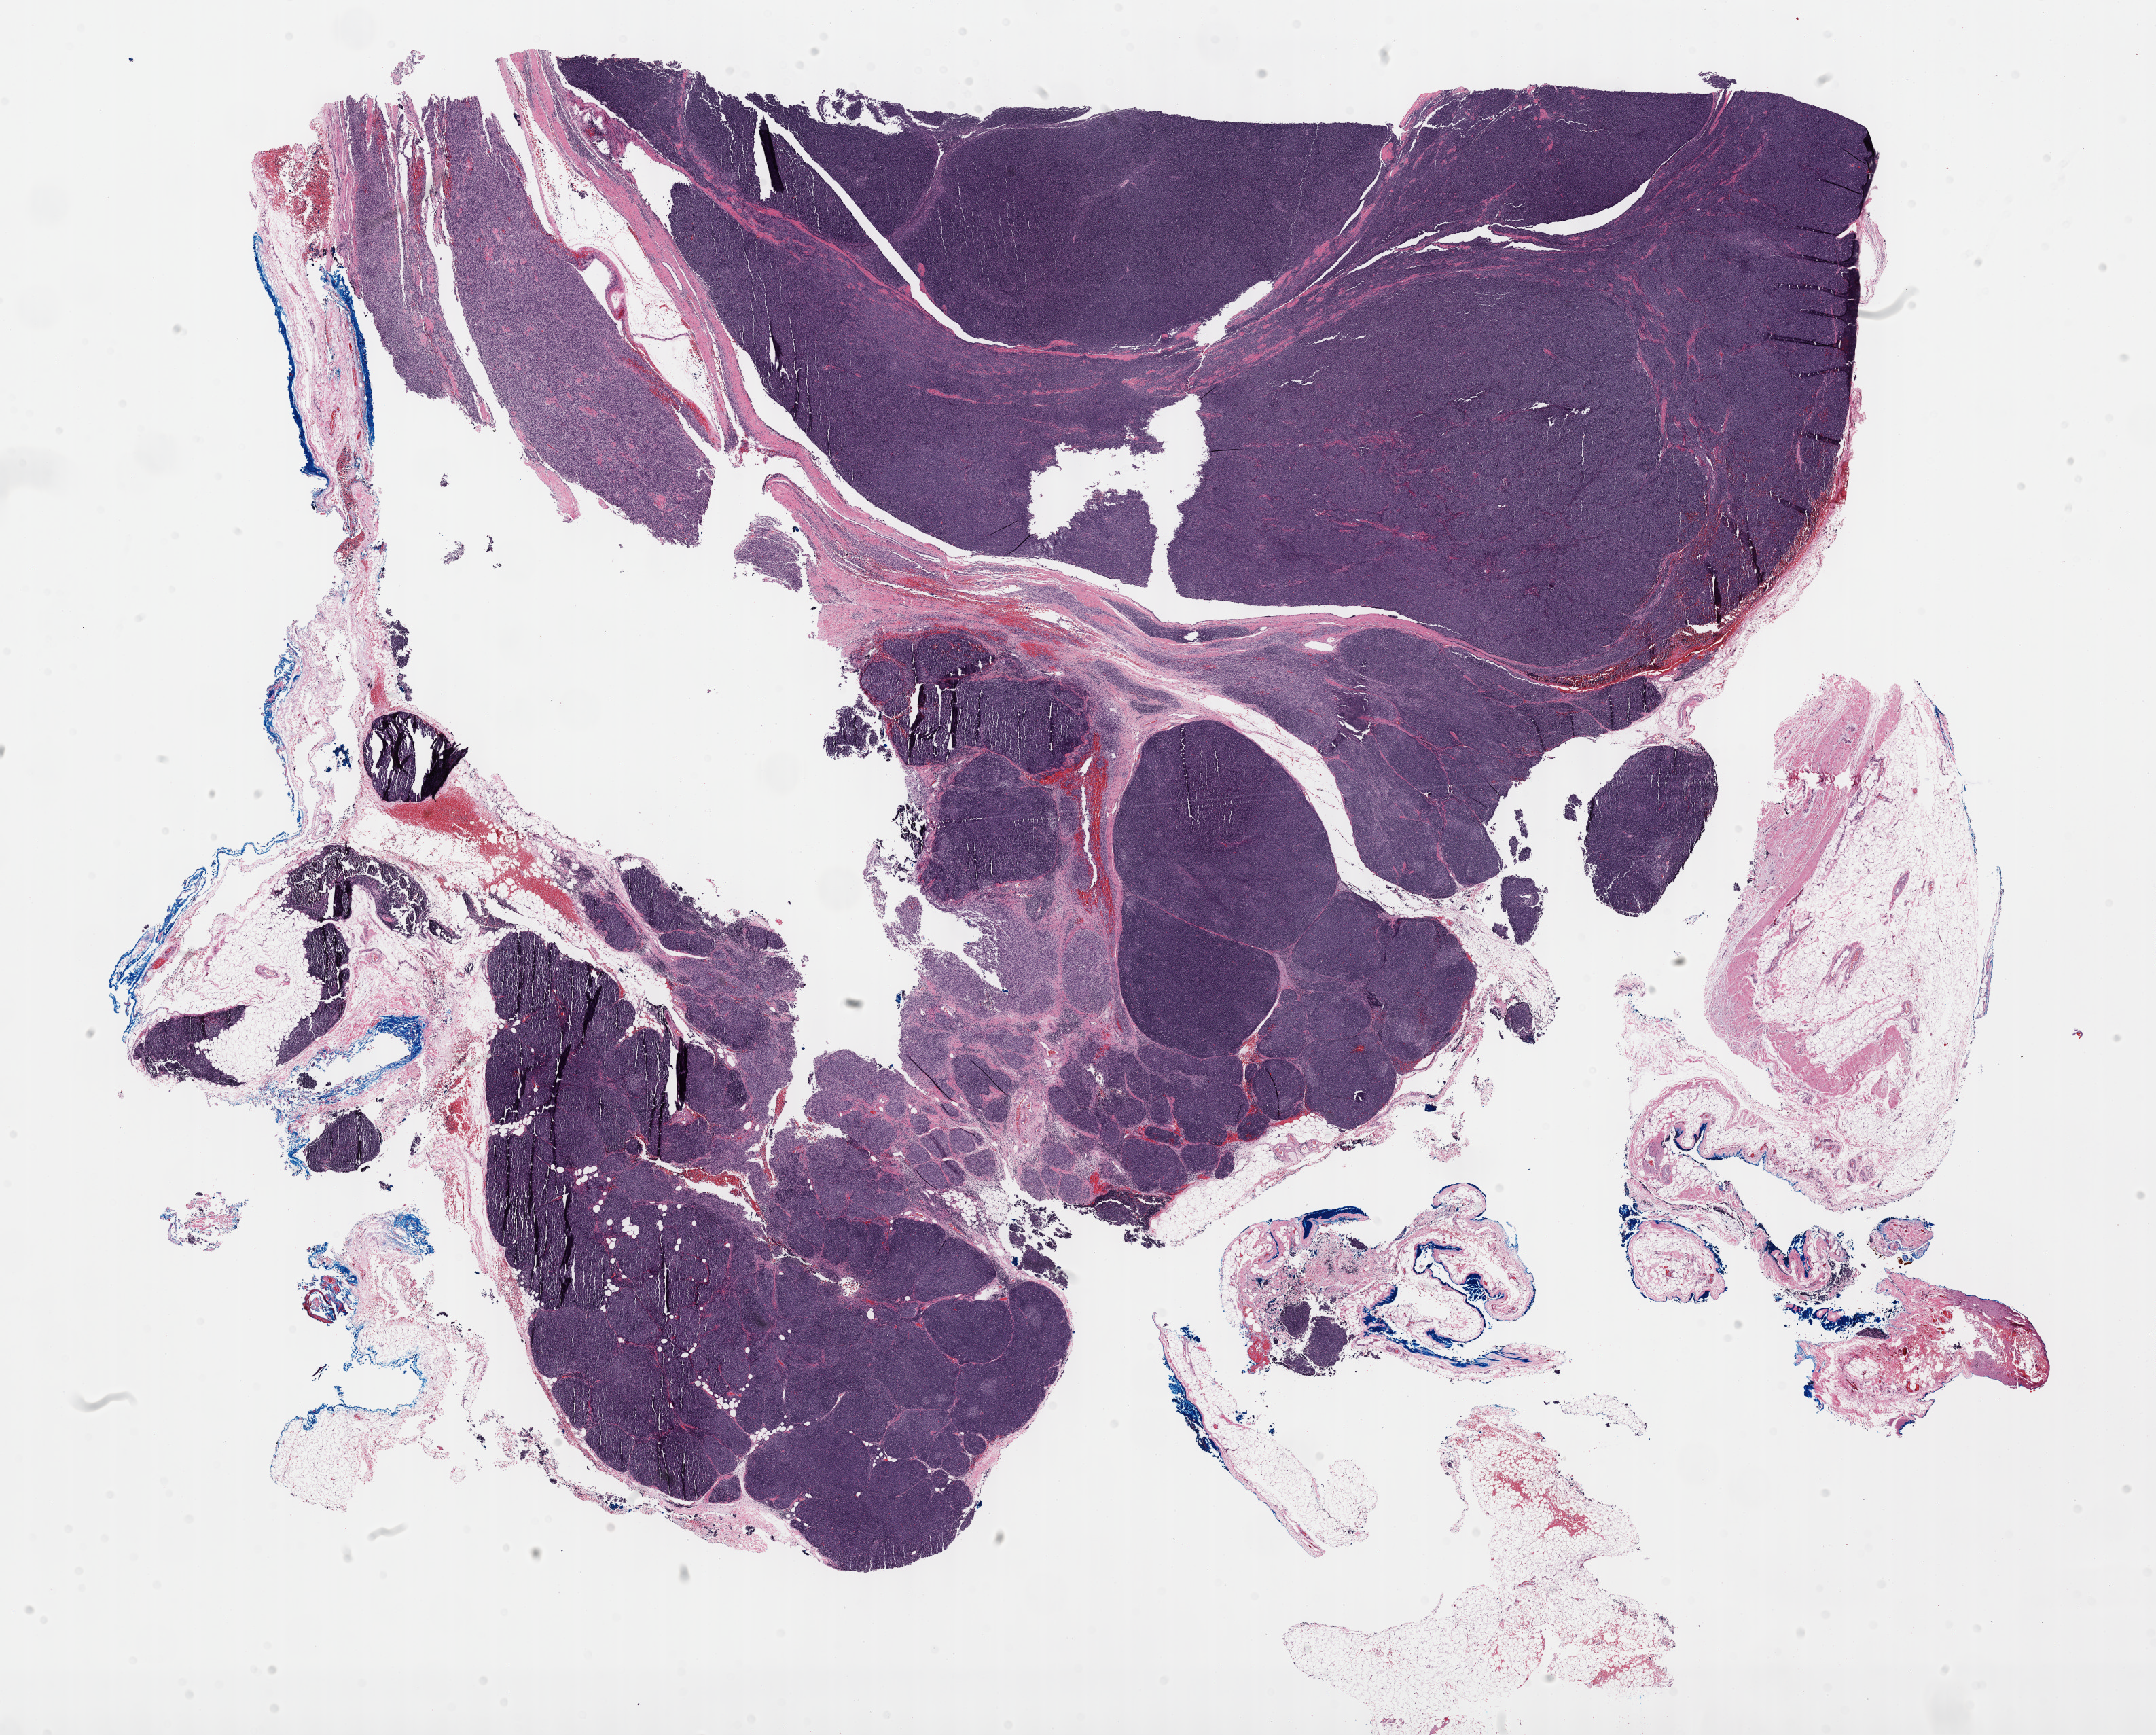
Whole-slide histology image, H&E-stained, whole scanned area (about 25.7 x 20.7 mm) shown as a low-resolution overview. FFPE section. Thymus, primary tumour sample. Patient: female, age at initial diagnosis 54 years.
* pathologic diagnosis: Thymoma, type AB, NOS